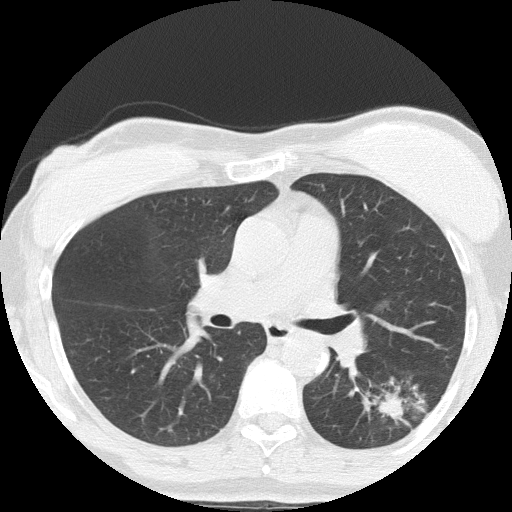
Low-dose screening chest CT, one axial slice. Slice 87 of 152 in the series (ordered by position). Reconstruction kernel FC51. 120 kVp. Lung window (W 1500 / L -600 HU). 2 mm slice thickness. 512 × 512 image matrix, field of view 308 × 308 mm.
Annotated regions visible in this slice (outlined manually by an expert reader):
- lesion 1 (tumor, lower lobe of left lung): bounding box <379,394,404,419> (left, top, right, bottom; pixels)